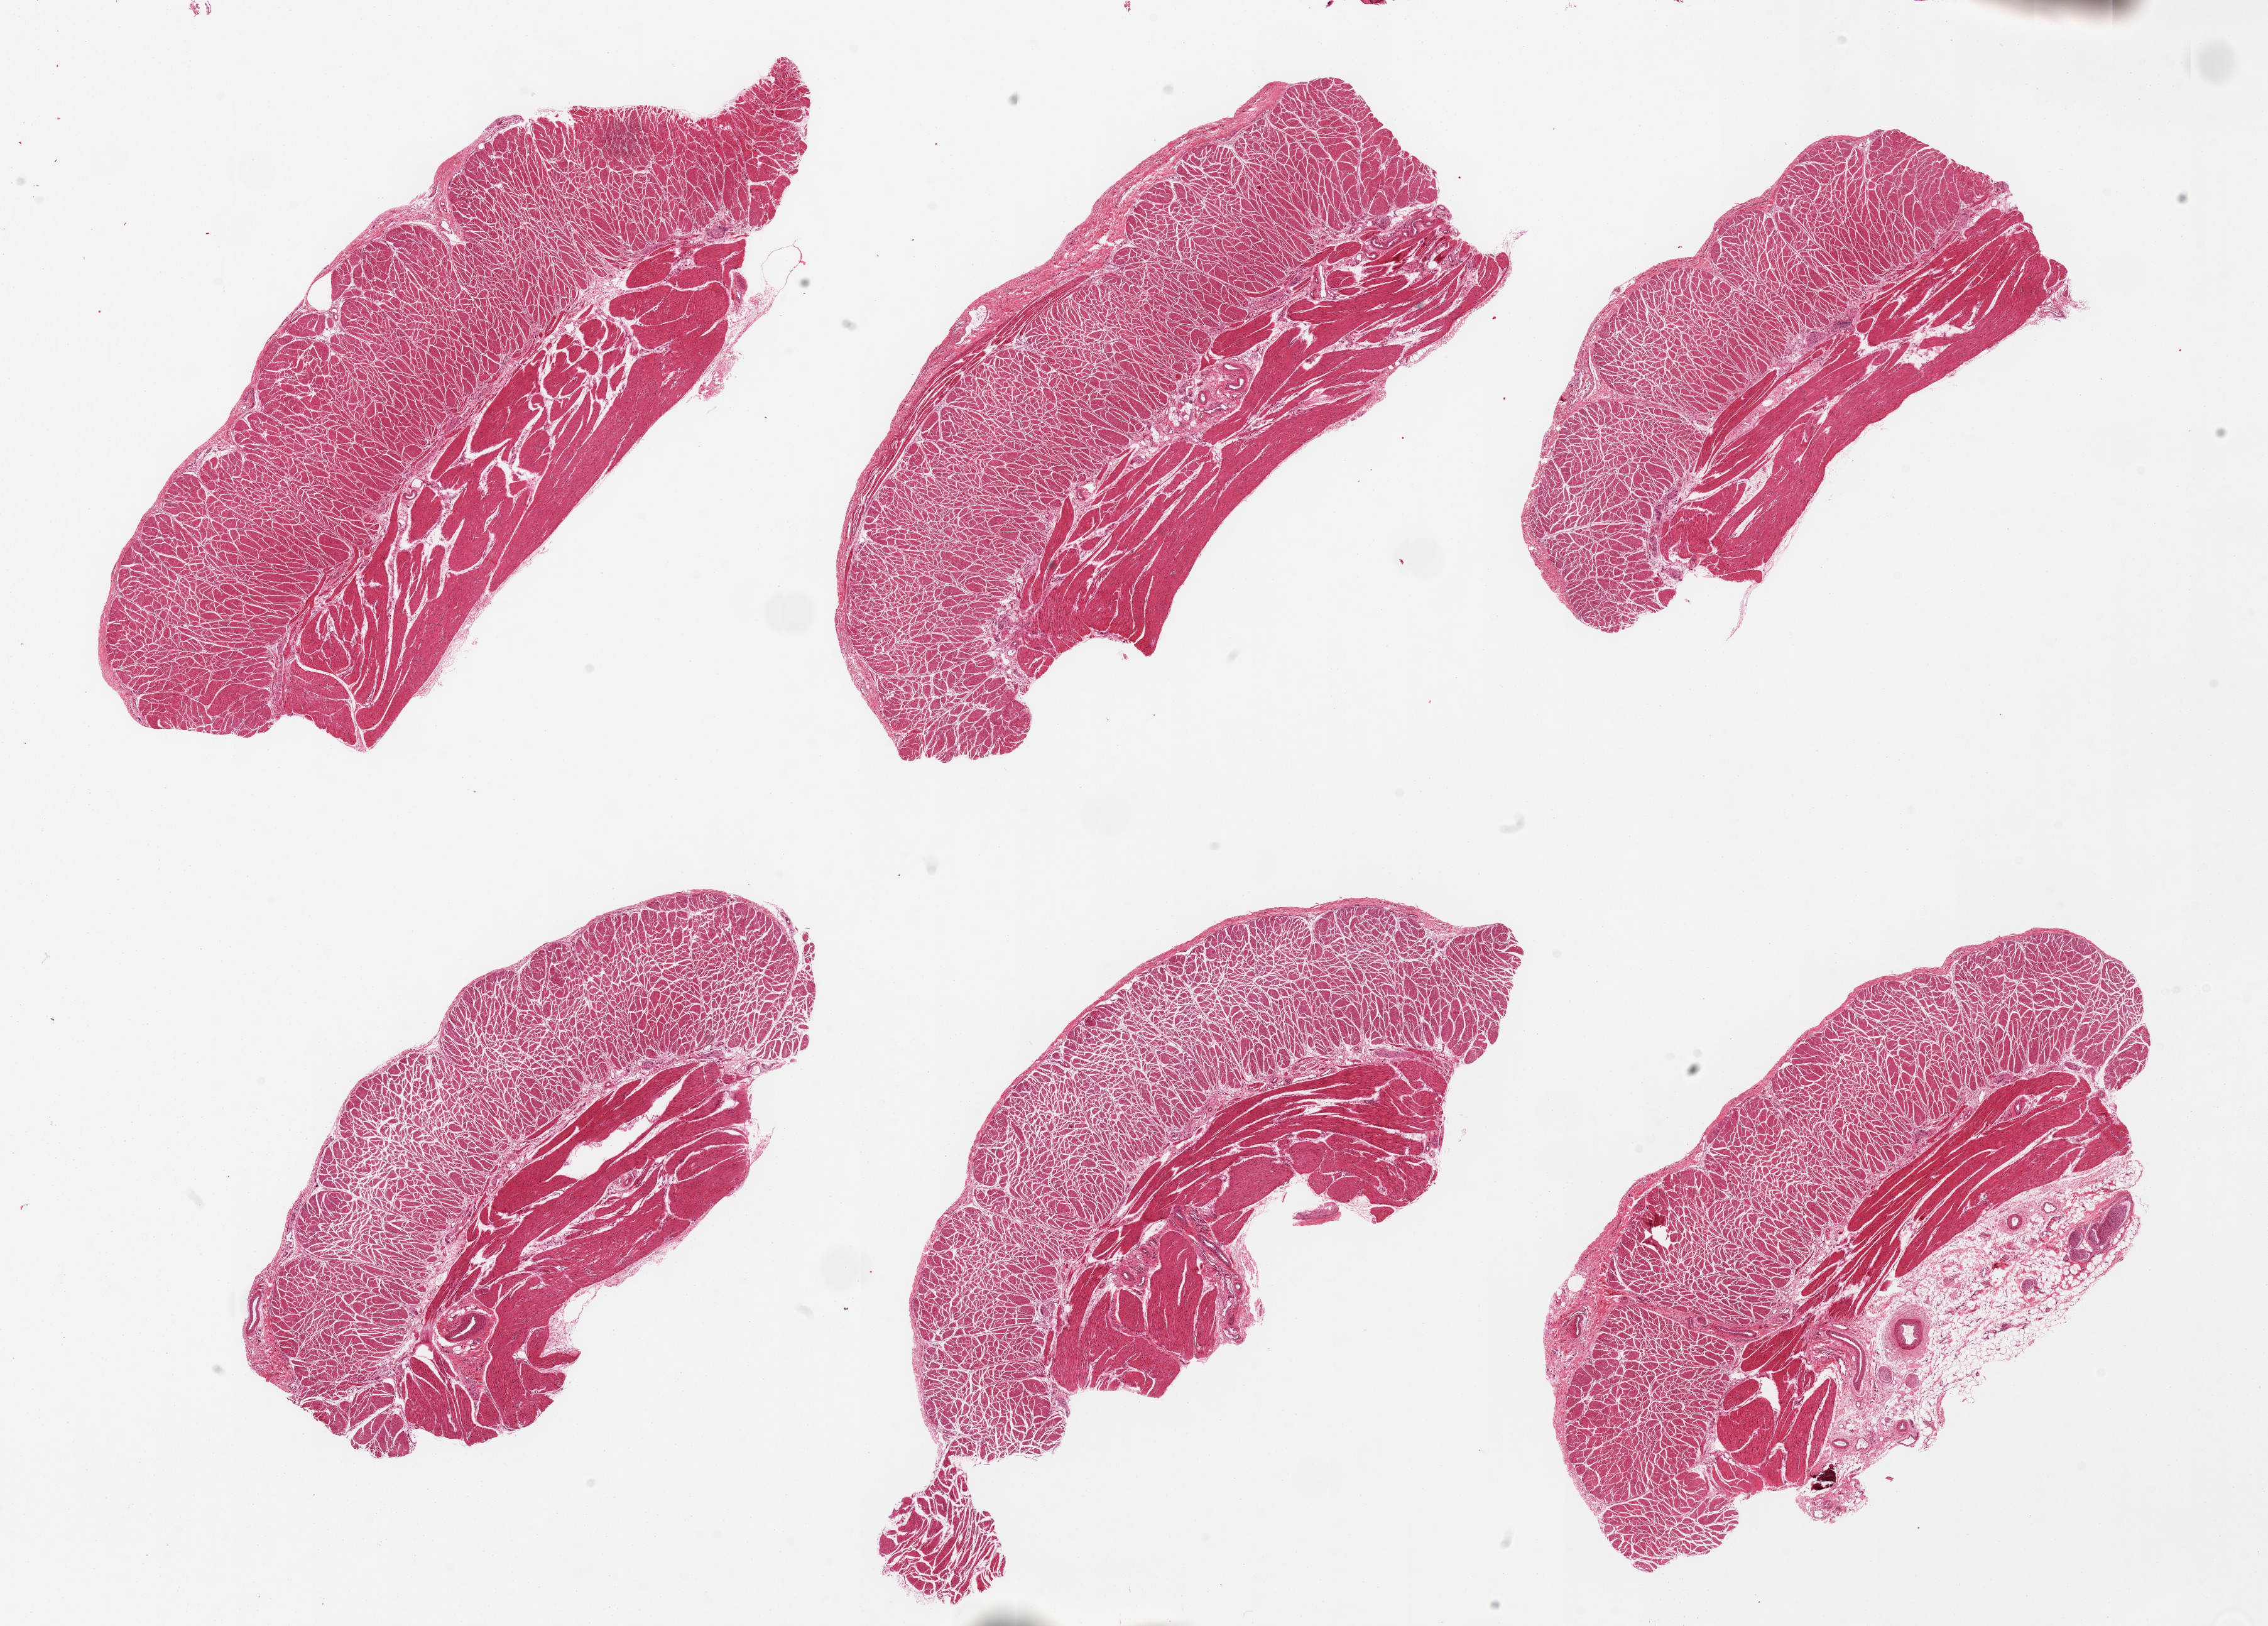
Whole-slide image, hematoxylin and eosin (H&E) stain — a low-resolution overview of the entire scanned area, about 28.5 x 20.5 mm (acquisition: 20x scan). PAXgene-fixed, paraffin-embedded tissue. Section of esophageal muscle (target tissue). Donor tissue sample.
- reviewer comment on this tissue sample: 6 pieces, well trimmed of mucosa